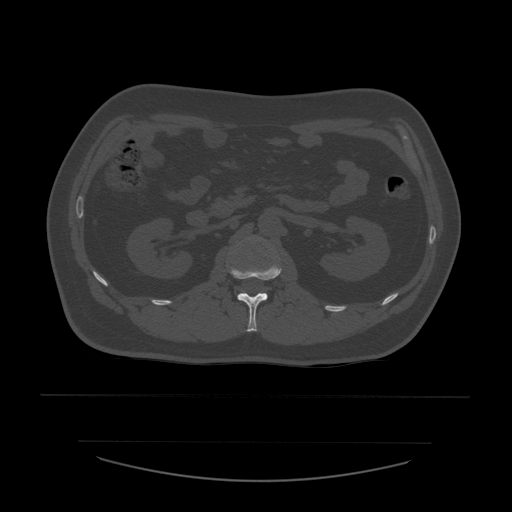
CT including the spine, one axial slice; slice 218 of 532 in the series (ordered by position); 120 kVp; bone window (W 1800 / L 400 HU); 1.25 mm slice thickness; 512 × 512 image matrix. Patient age 44 years. Case-level facts recorded for this patient, not image findings: primary cancer: soft tissue sarcoma.
Annotated regions visible in this slice (semi-automatic segmentation, software-assisted and operator-edited):
- L1 vertebra: box from (x=230, y=264) to (x=282, y=332) px